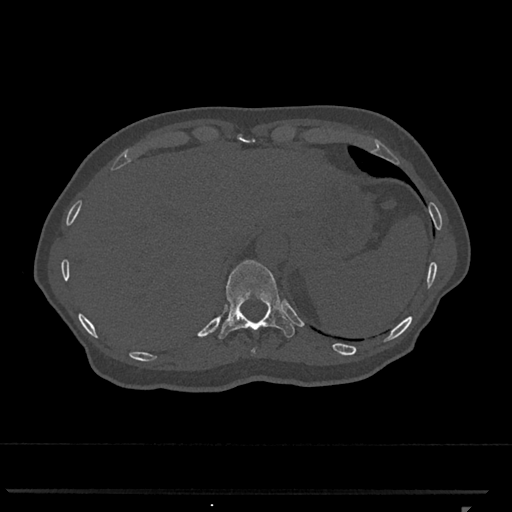
CT including the spine, one axial slice; slice 524 of 793 in the series (ordered by position); 120 kVp; bone window (W 1800 / L 400 HU); 0.5 mm slice thickness; 512 × 512 image matrix, field of view 380 × 380 mm. Female patient, age 62 years. Case-level facts recorded for this patient, not image findings: primary cancer: renal.
Structures marked on this image (semi-automatic segmentation, software-assisted and operator-edited):
- T10 vertebra: box from (x=251, y=349) to (x=256, y=353) px
- T11 vertebra: (x=218, y=260)–(x=295, y=339)